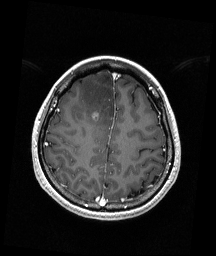
Brain MRI from a brain-tumour surgery series, one axial slice. Position 54 of 192 along the scan axis. T1-weighted post-contrast. 1 mm slice thickness. 216 × 256 image matrix, field of view 211 × 250 mm. Case-level facts recorded for this patient, not image findings: histopathology: Astrocytoma; WHO grade: 4; IDH mutation: yes; tumour location: Right Frontal.
Outlined on this slice (outlined manually by an expert reader):
- tumour: bounding box [x1, y1, x2, y2] px = [92, 111, 99, 121]